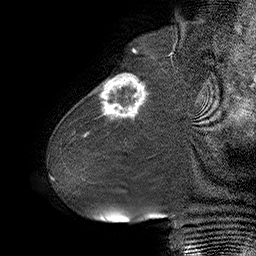
Breast MRI (dynamic contrast-enhanced), one sagittal slice. Slice 14 of 55 in the series (ordered by position). Dynamic contrast-enhanced series, time point 2 of 6 at this slice position (early post-contrast). 1.5 T. TE 4.5 ms, TR 32.4 ms. 3 mm slice thickness. 256 × 256 image matrix, field of view 180 × 180 mm. Female patient. Case-level facts recorded for this patient, not image findings: setting: breast cancer imaged before/during neoadjuvant chemotherapy; receptor status: HER2-positive.
Outlined on this slice (semi-automatic segmentation, software-assisted and operator-edited):
- analysis volume of interest (the breast-tissue region the enhancement analysis was run in; not a lesion): bounding box [x1, y1, x2, y2] px = [80, 64, 163, 134]
- tumour enhancement mask (voxels above the 100 % enhancement threshold inside the analysis volume of interest): [99, 74, 148, 120]